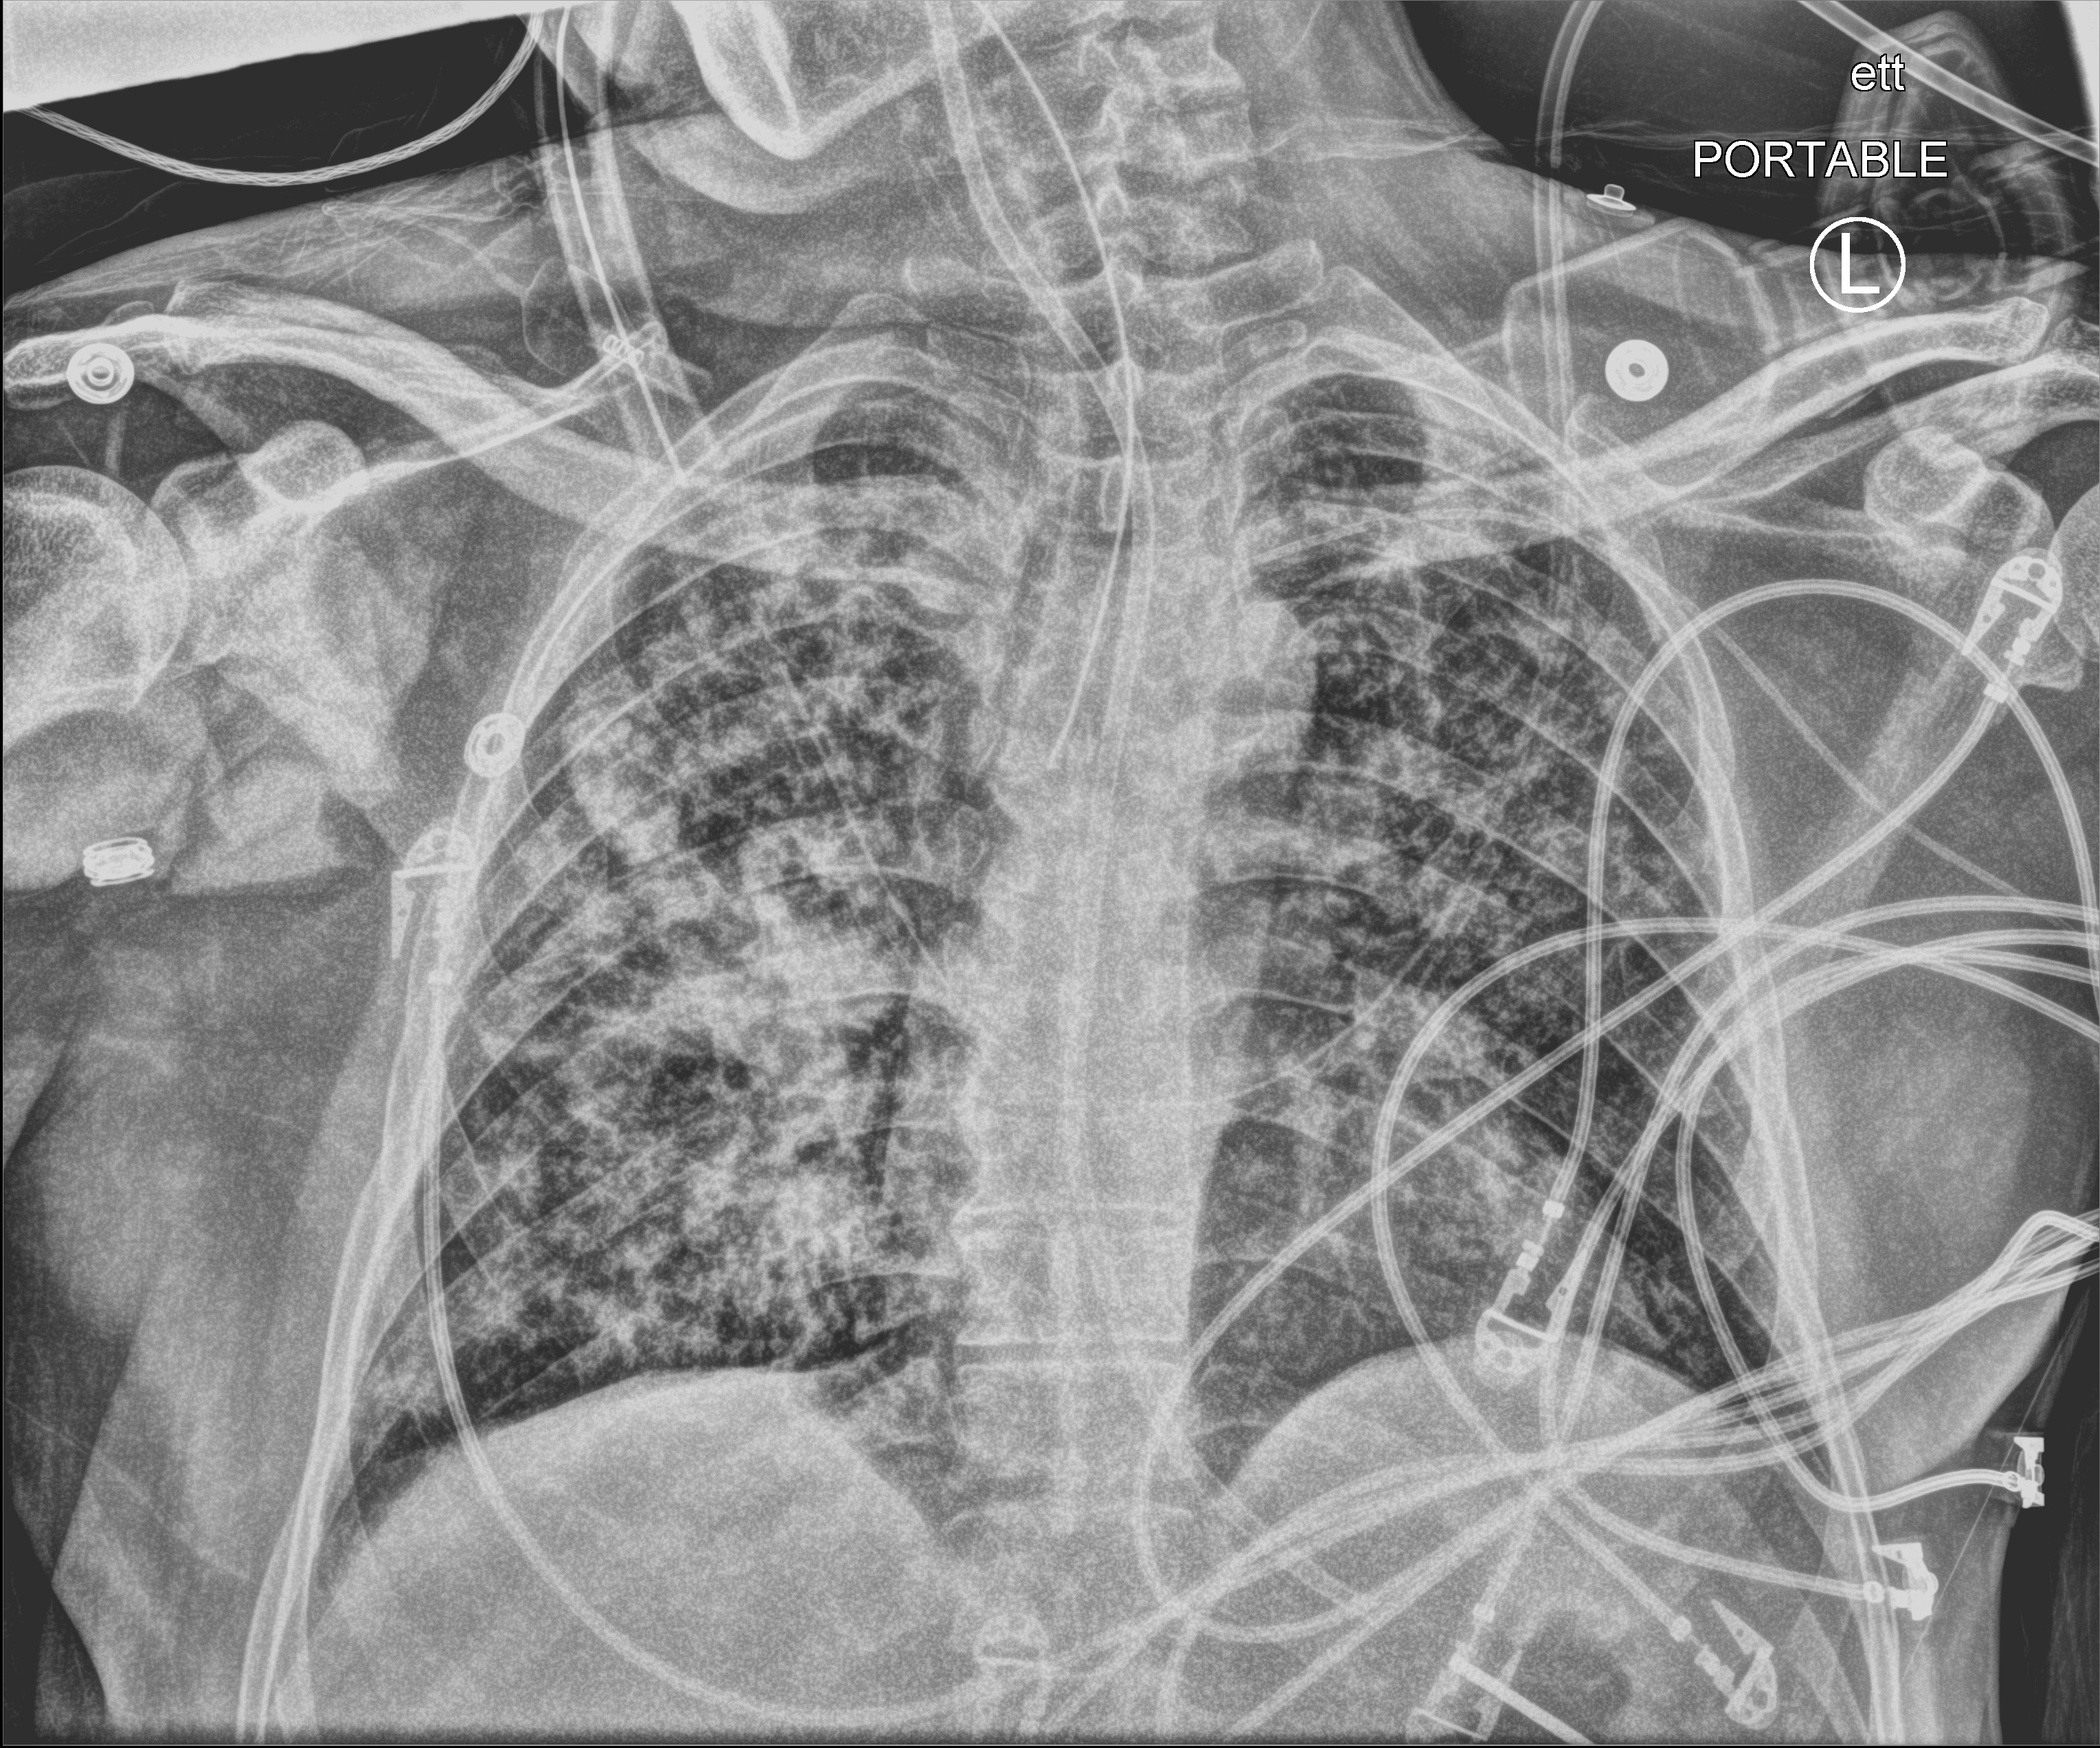
Chest X-ray (portable), anteroposterior (AP) projection. Patient hospitalised with COVID-19; male, aged 18–59 years.
Admission-level facts for this patient (not findings on this image; timing relative to this image not recorded):
- chronic kidney disease (admission record): no
- admitted to intensive care during this hospital stay: yes